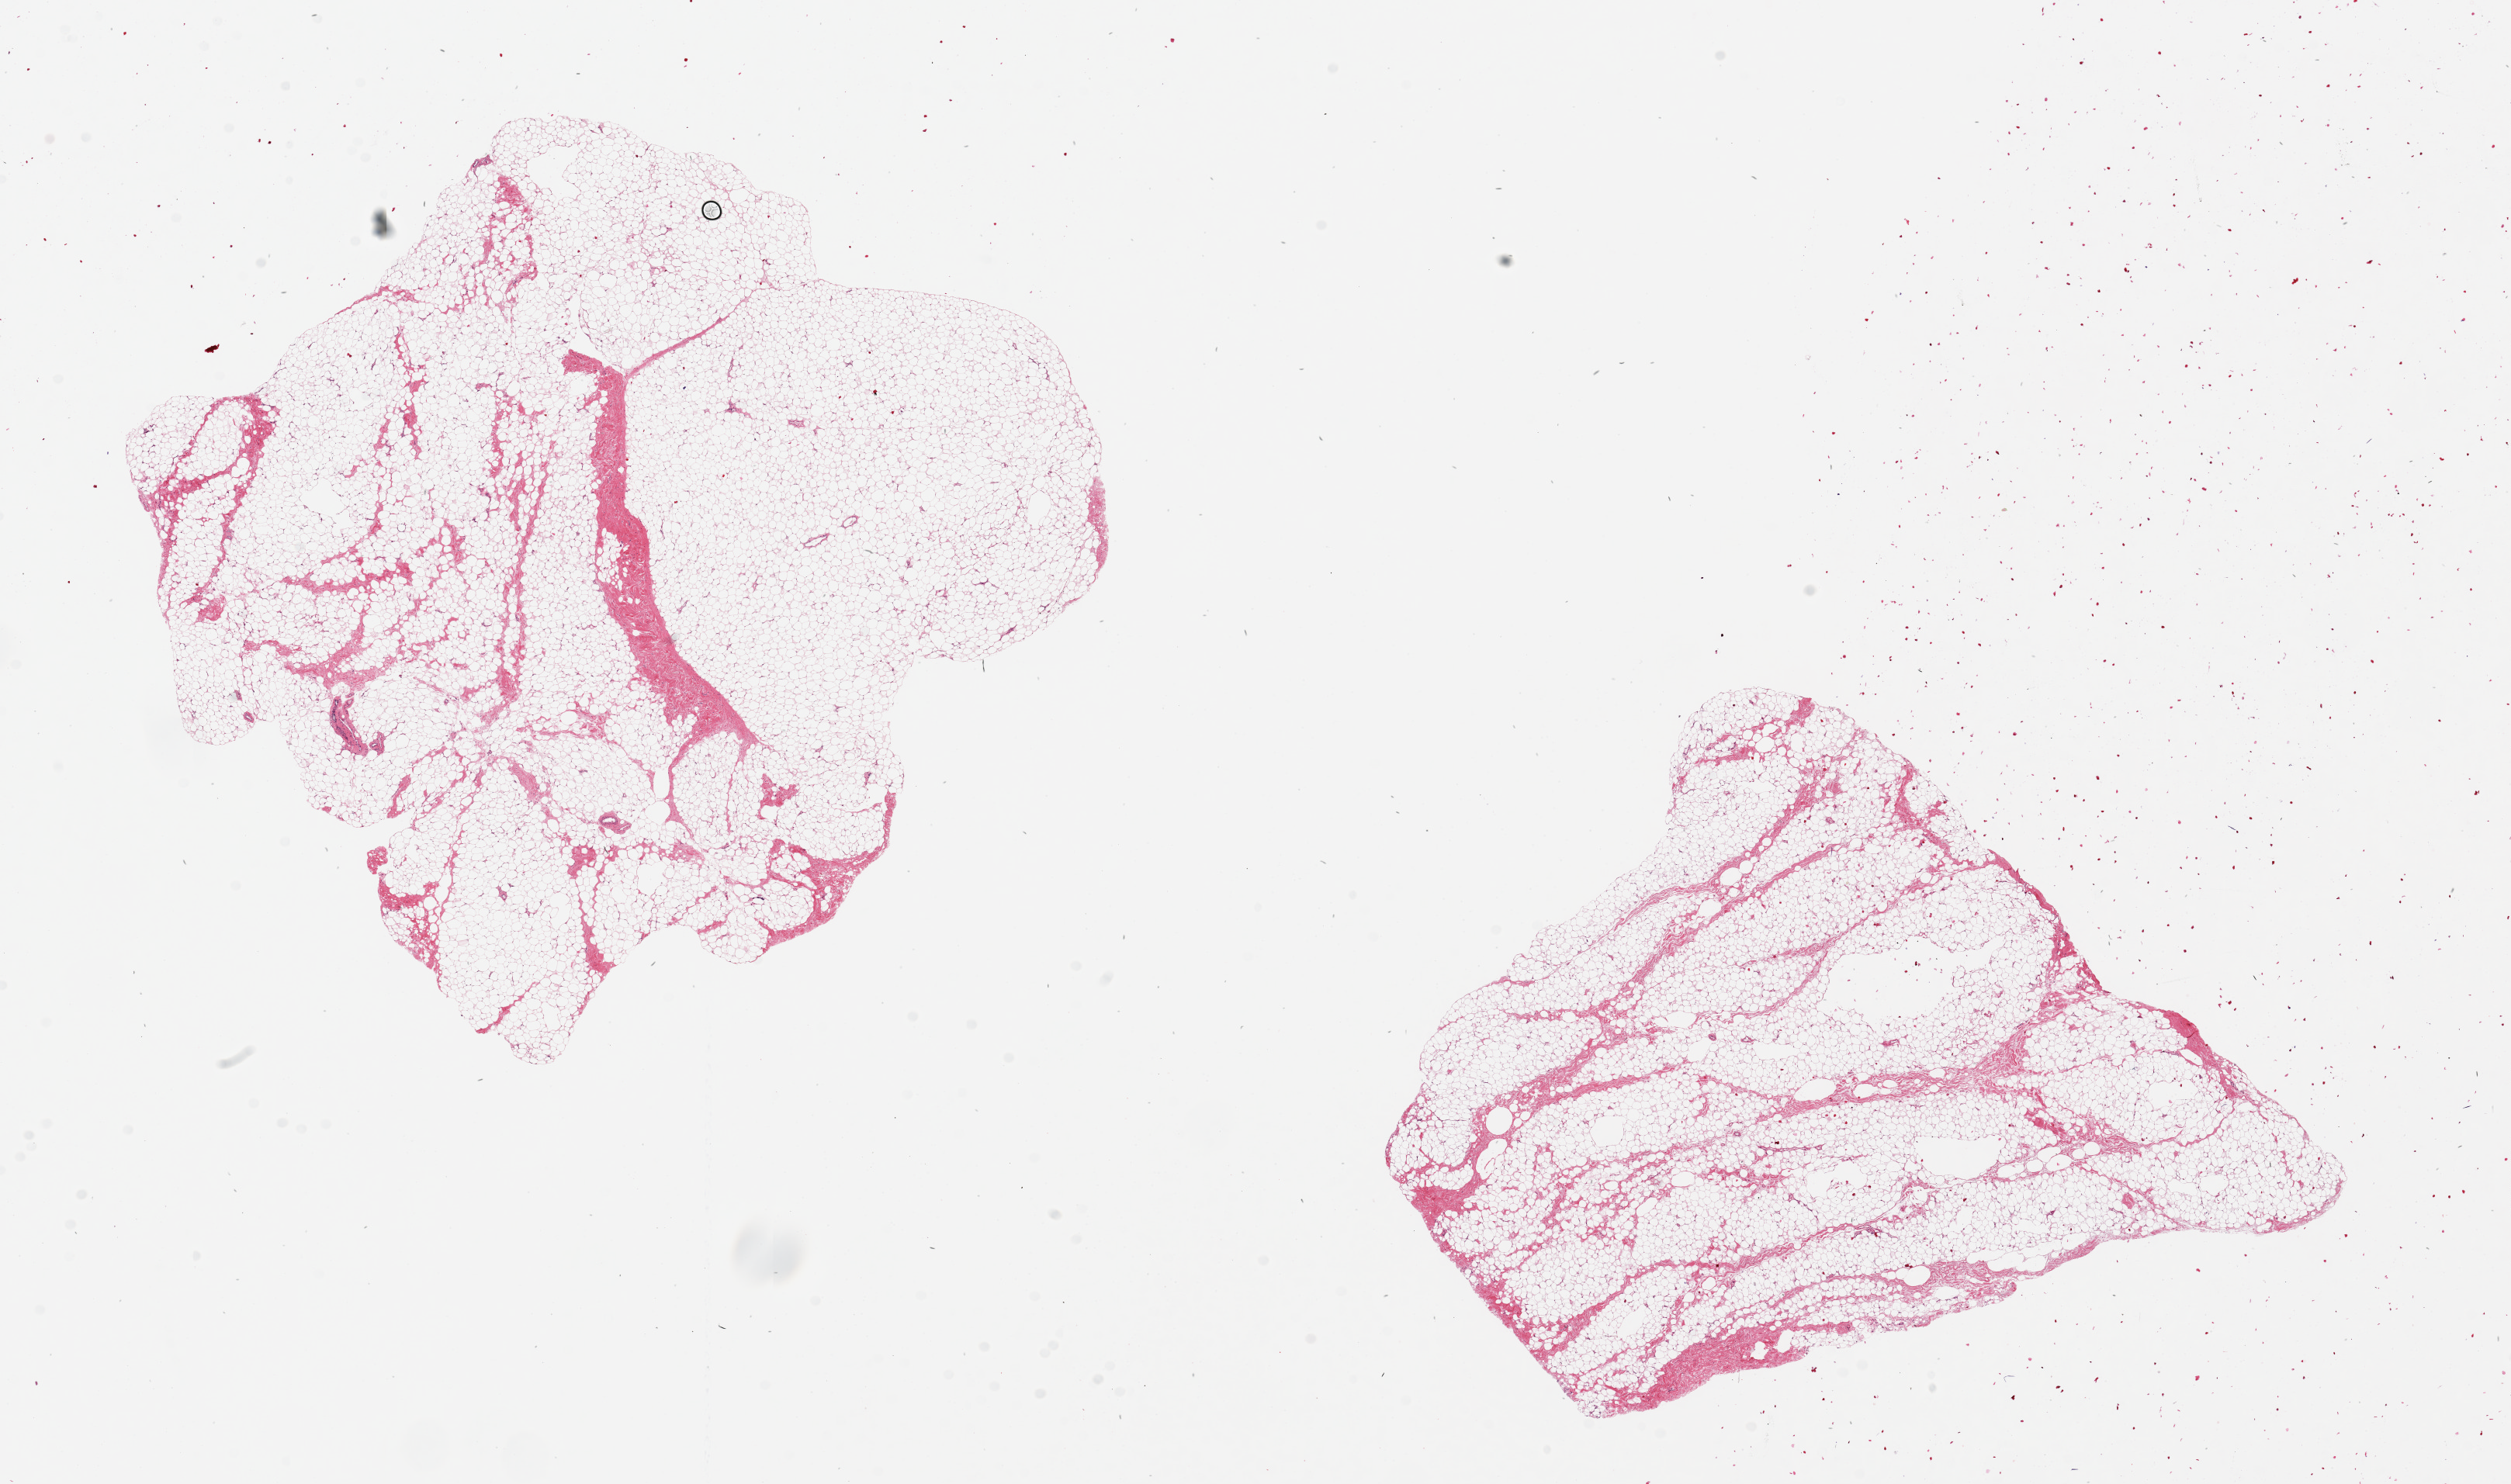
Whole-slide image, haematoxylin and eosin stain — shown as a low-resolution overview of the whole scanned area (about 25.6 x 15.1 mm); PAXgene-fixed, paraffin-embedded tissue; target tissue: breast; tissue donor sample.
- pathologist's review note for this sample: 2 pieces, 9x8 & 8x8mm; all adipose, no mammary tissue; a few small defects